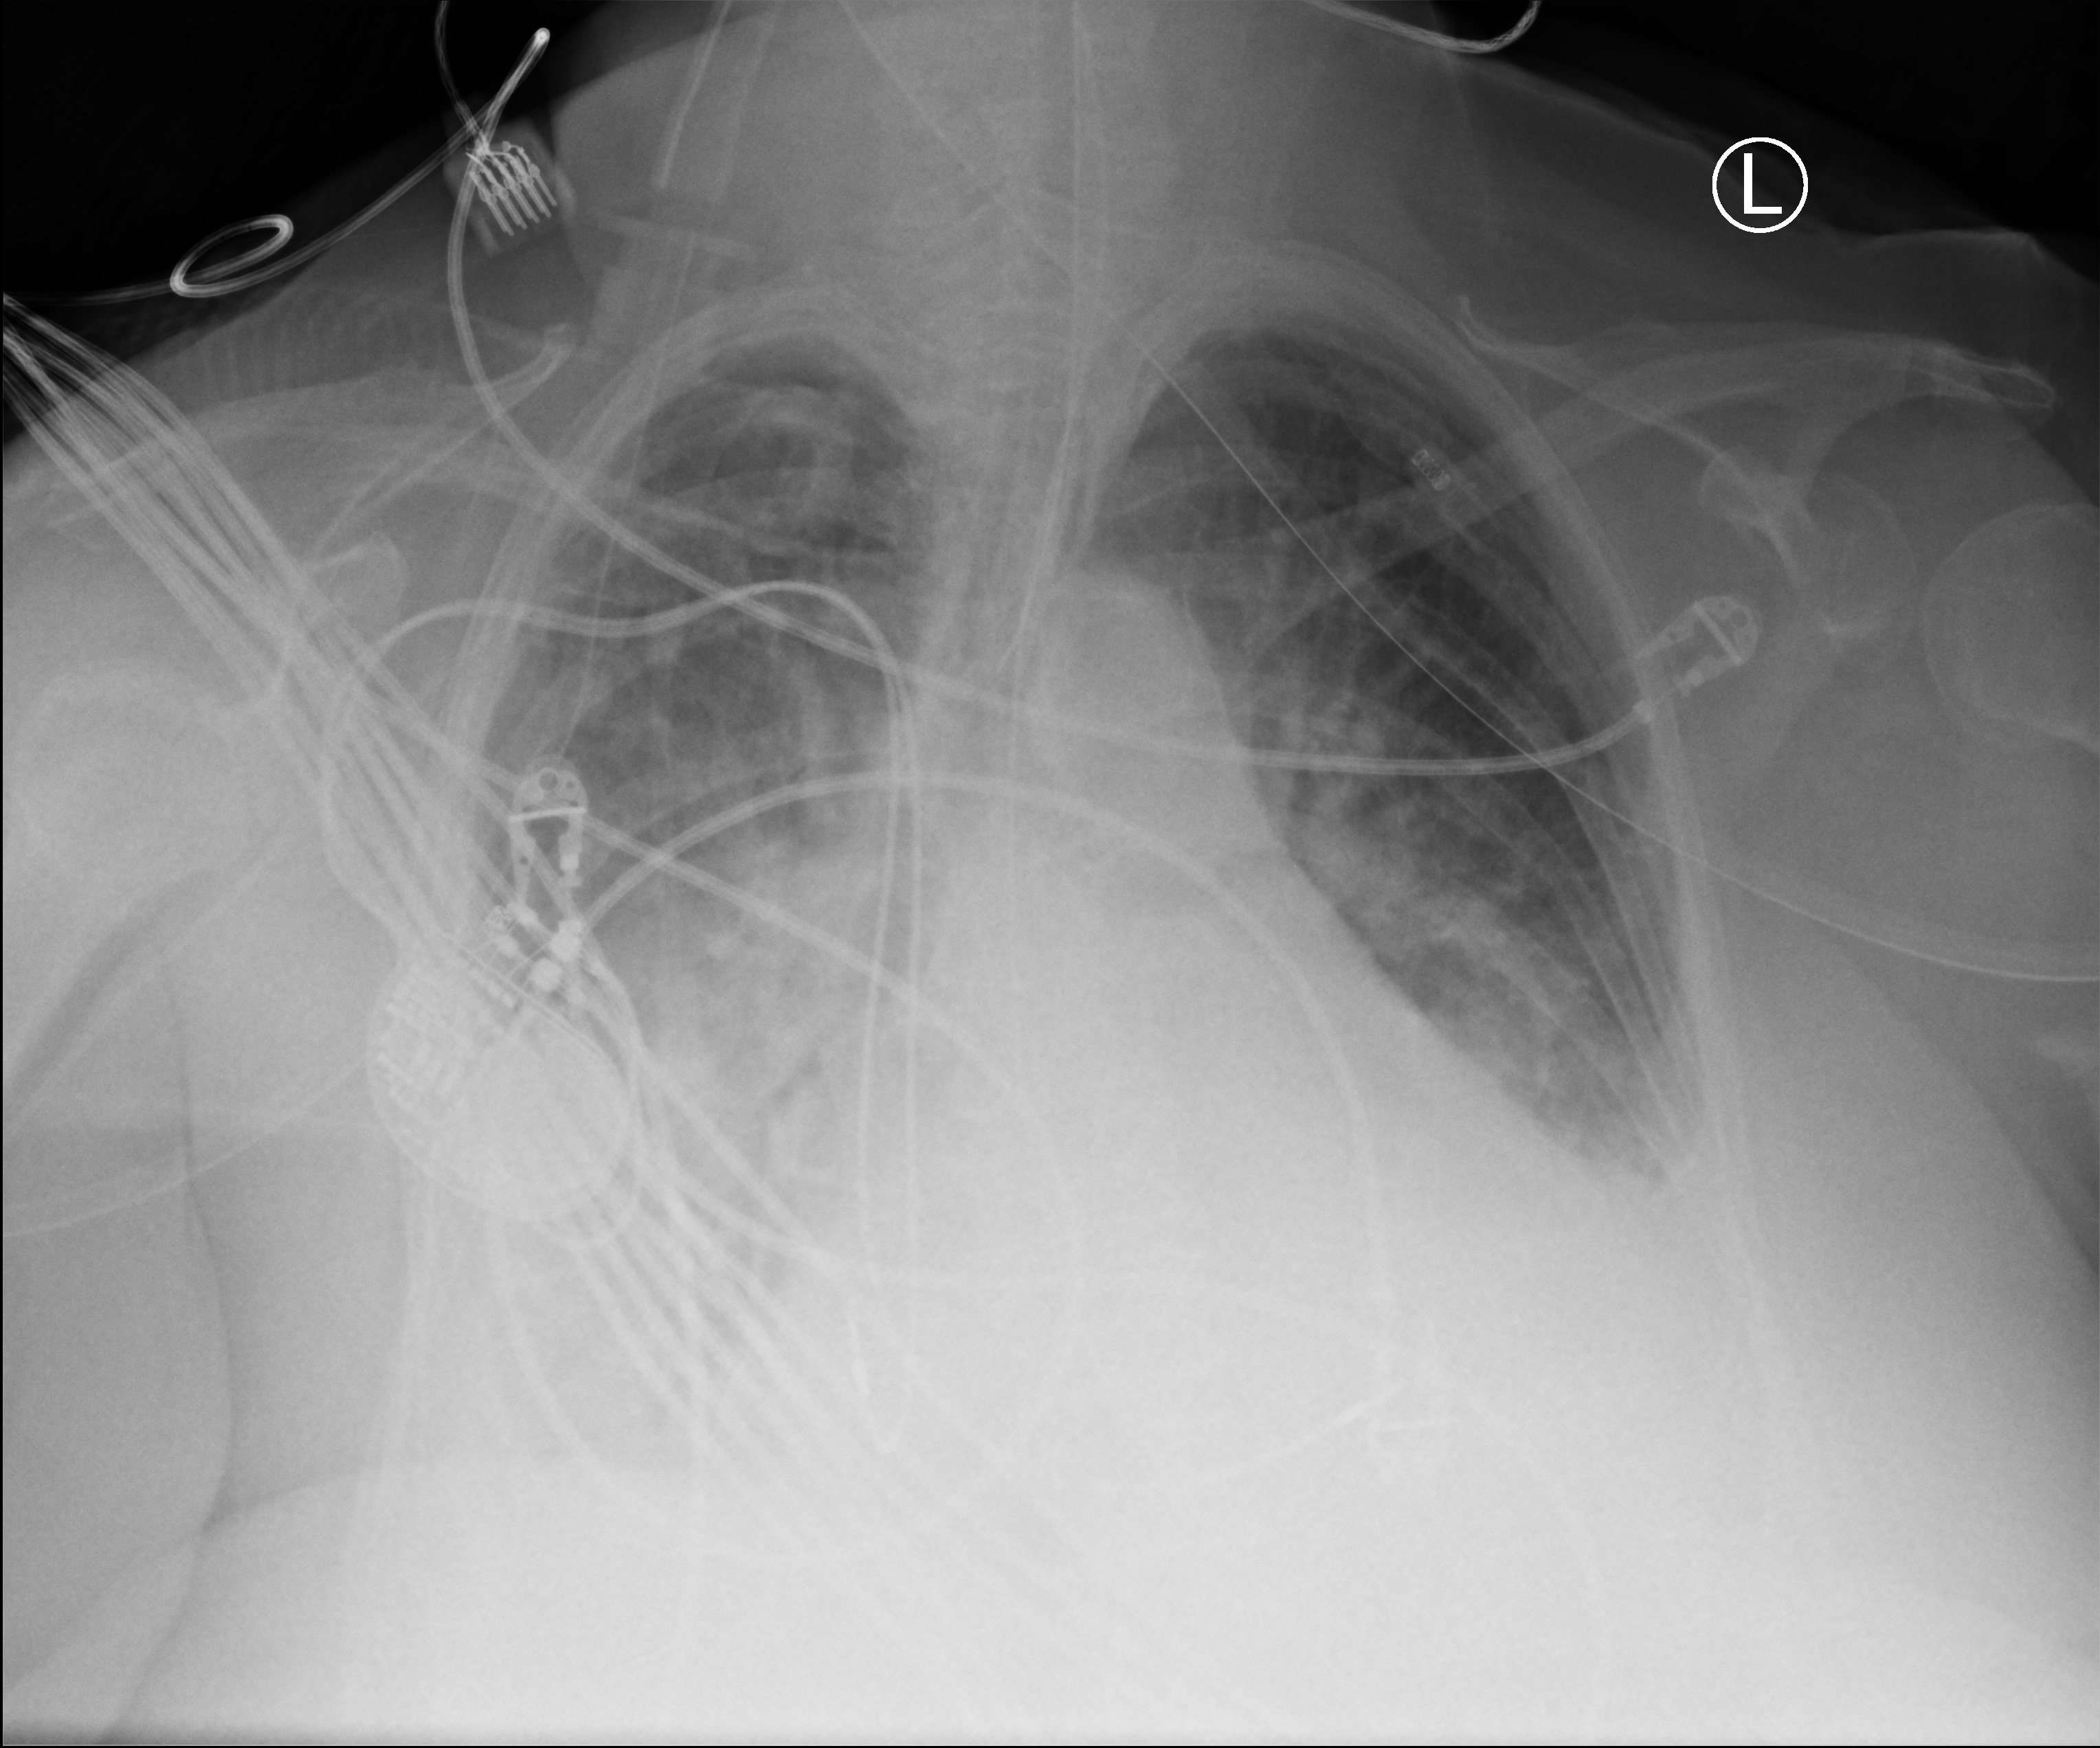
Chest X-ray (portable); anteroposterior (AP) projection. Patient hospitalised with COVID-19; female, aged 75–90 years.
From the hospital-stay record, not from the radiograph (when in the stay this image was taken is not recorded): mechanically ventilated during this hospital stay: yes; other chronic lung disease (admission record): yes; admitted to intensive care during this hospital stay: yes.